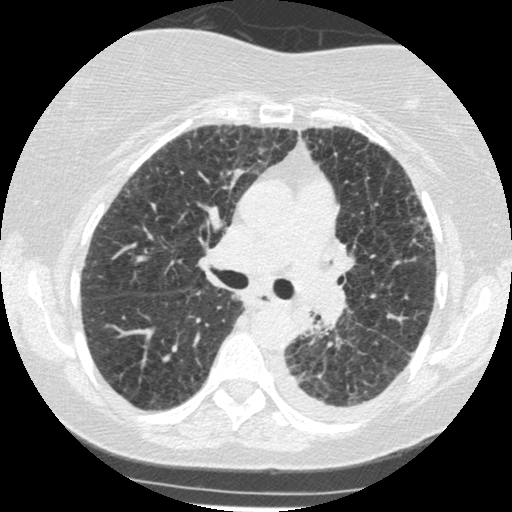
Low-dose screening chest CT, one axial slice. Position 165 of 341 along the scan axis. Reconstruction kernel STANDARD. Lung window (W 1500 / L -600 HU). 1.25 mm slice thickness. 512 × 512 image matrix.
Outlined on this slice (manually delineated by an expert):
- lesion 1 (tumor, lower lobe of left lung): bounding box (x1, y1, x2, y2) in pixels: (296, 309, 314, 334)